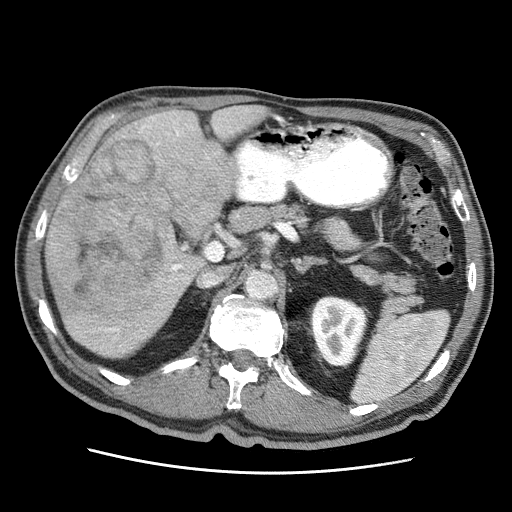
Contrast-enhanced abdominal CT (liver protocol), one axial slice; position 23 of 75 along the scan axis; reconstruction kernel STANDARD; soft-tissue window (W 400 / L 40 HU); 2.5 mm slice thickness; 512 × 512 image matrix, field of view 360 × 360 mm. Case-level facts recorded for this patient, not image findings: diagnosis: hepatocellular carcinoma (patient treated with transarterial chemoembolisation; whether this scan precedes or follows treatment is not stated here); TNM stage (as recorded): Stage-IIIA; Child-Pugh class: A; tumour differentiation: well differentiated; tumour size: 13.9 cm.
Structures marked on this image (semi-automatic segmentation, software-assisted and operator-edited):
- liver parenchyma outside the tumour (the mass and vessels are separate outlines, so this box may not span the whole liver): bounding box (x1, y1, x2, y2) in pixels: (46, 106, 266, 358)
- mass: (47, 138, 223, 324)
- liver vessels: (98, 116, 232, 332)